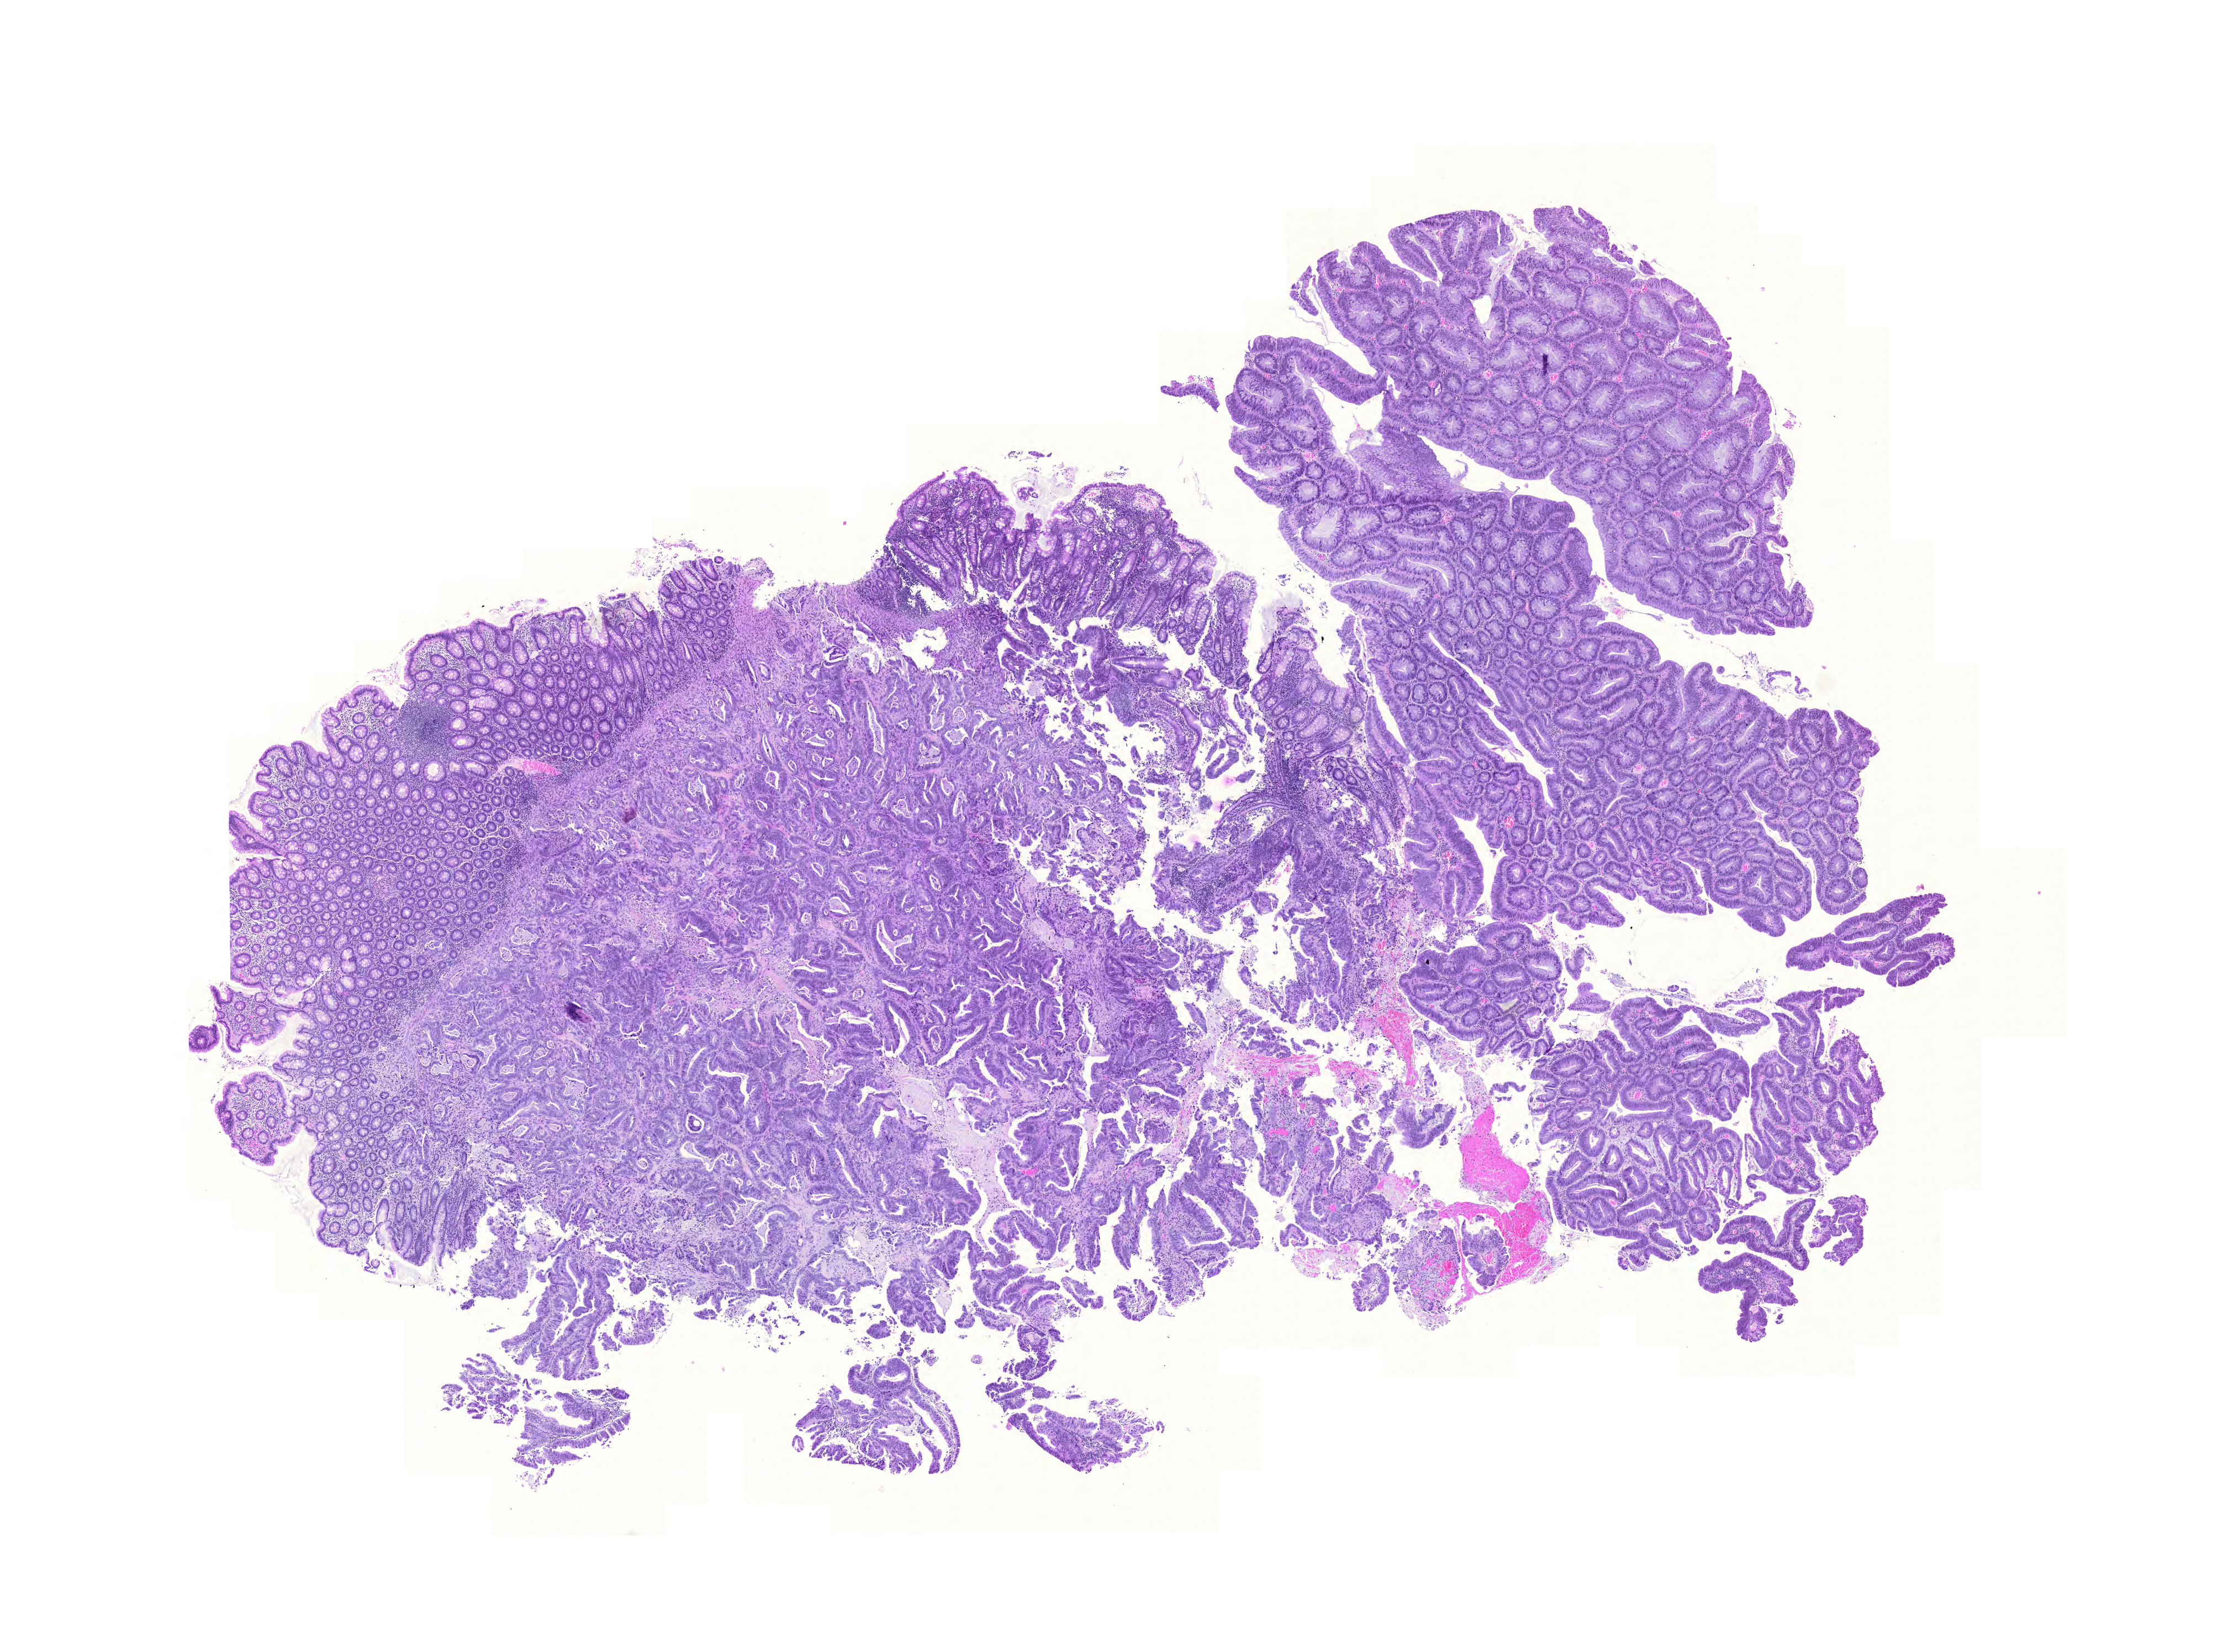
Whole-slide histology image, Hematoxylin and eosin (H&E) stained — low-resolution overview of the scanned area, about 14.9 x 11.1 mm (slide scanned at 20x), formalin-fixed paraffin-embedded (FFPE) diagnostic section, sample: primary tumour, colon. Female patient; age at initial diagnosis 67 years.
Lymph nodes positive (case pathology): 12 of 35 examined. Histologic diagnosis: Adenocarcinoma, NOS. TNM: T4 N2 M1. AJCC pathologic stage: IV (6th edition).